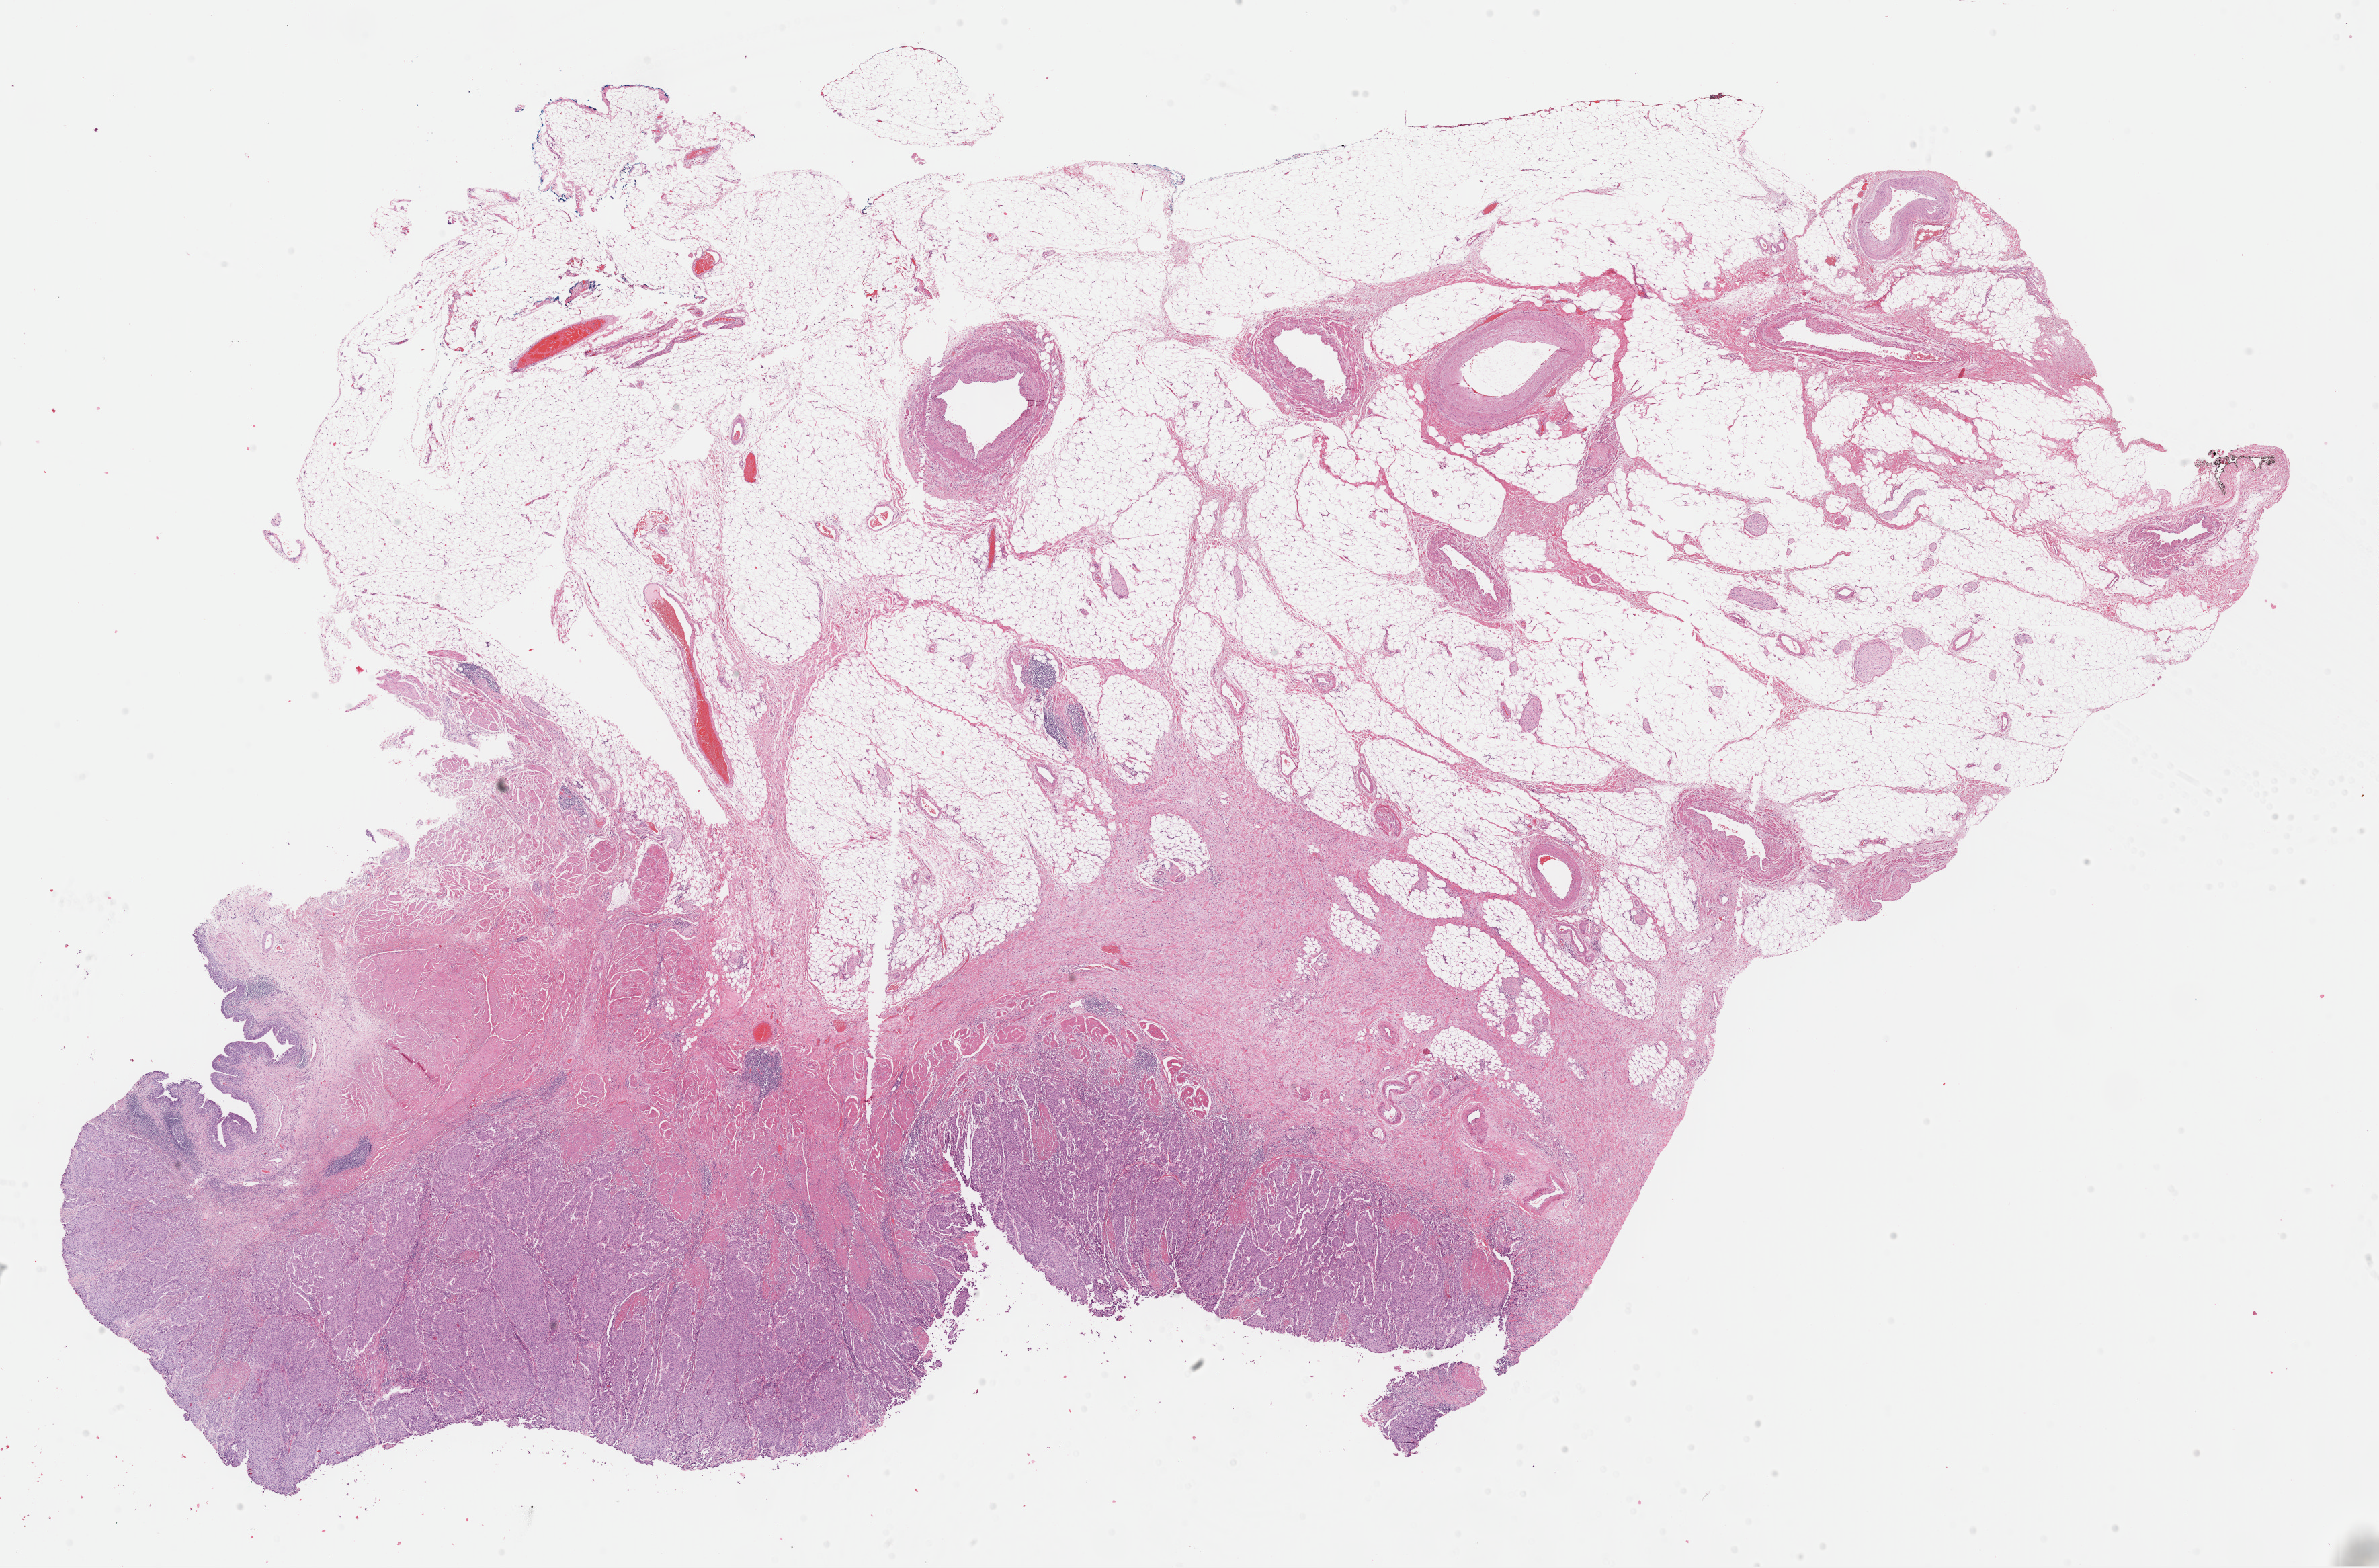
Whole-slide histology image, Hematoxylin and eosin (H&E) stained, shown as a low-resolution overview of the whole scanned area (about 28.0 x 18.4 mm, acquisition: 40x scan). FFPE section. Bladder, primary tumour sample. Female, age 61 years at initial diagnosis. Histologic grade: high grade.
• TNM: T2b N1 MX
• AJCC pathologic stage: IV (6th edition)
• histologic diagnosis: Transitional cell carcinoma (lateral wall of bladder)